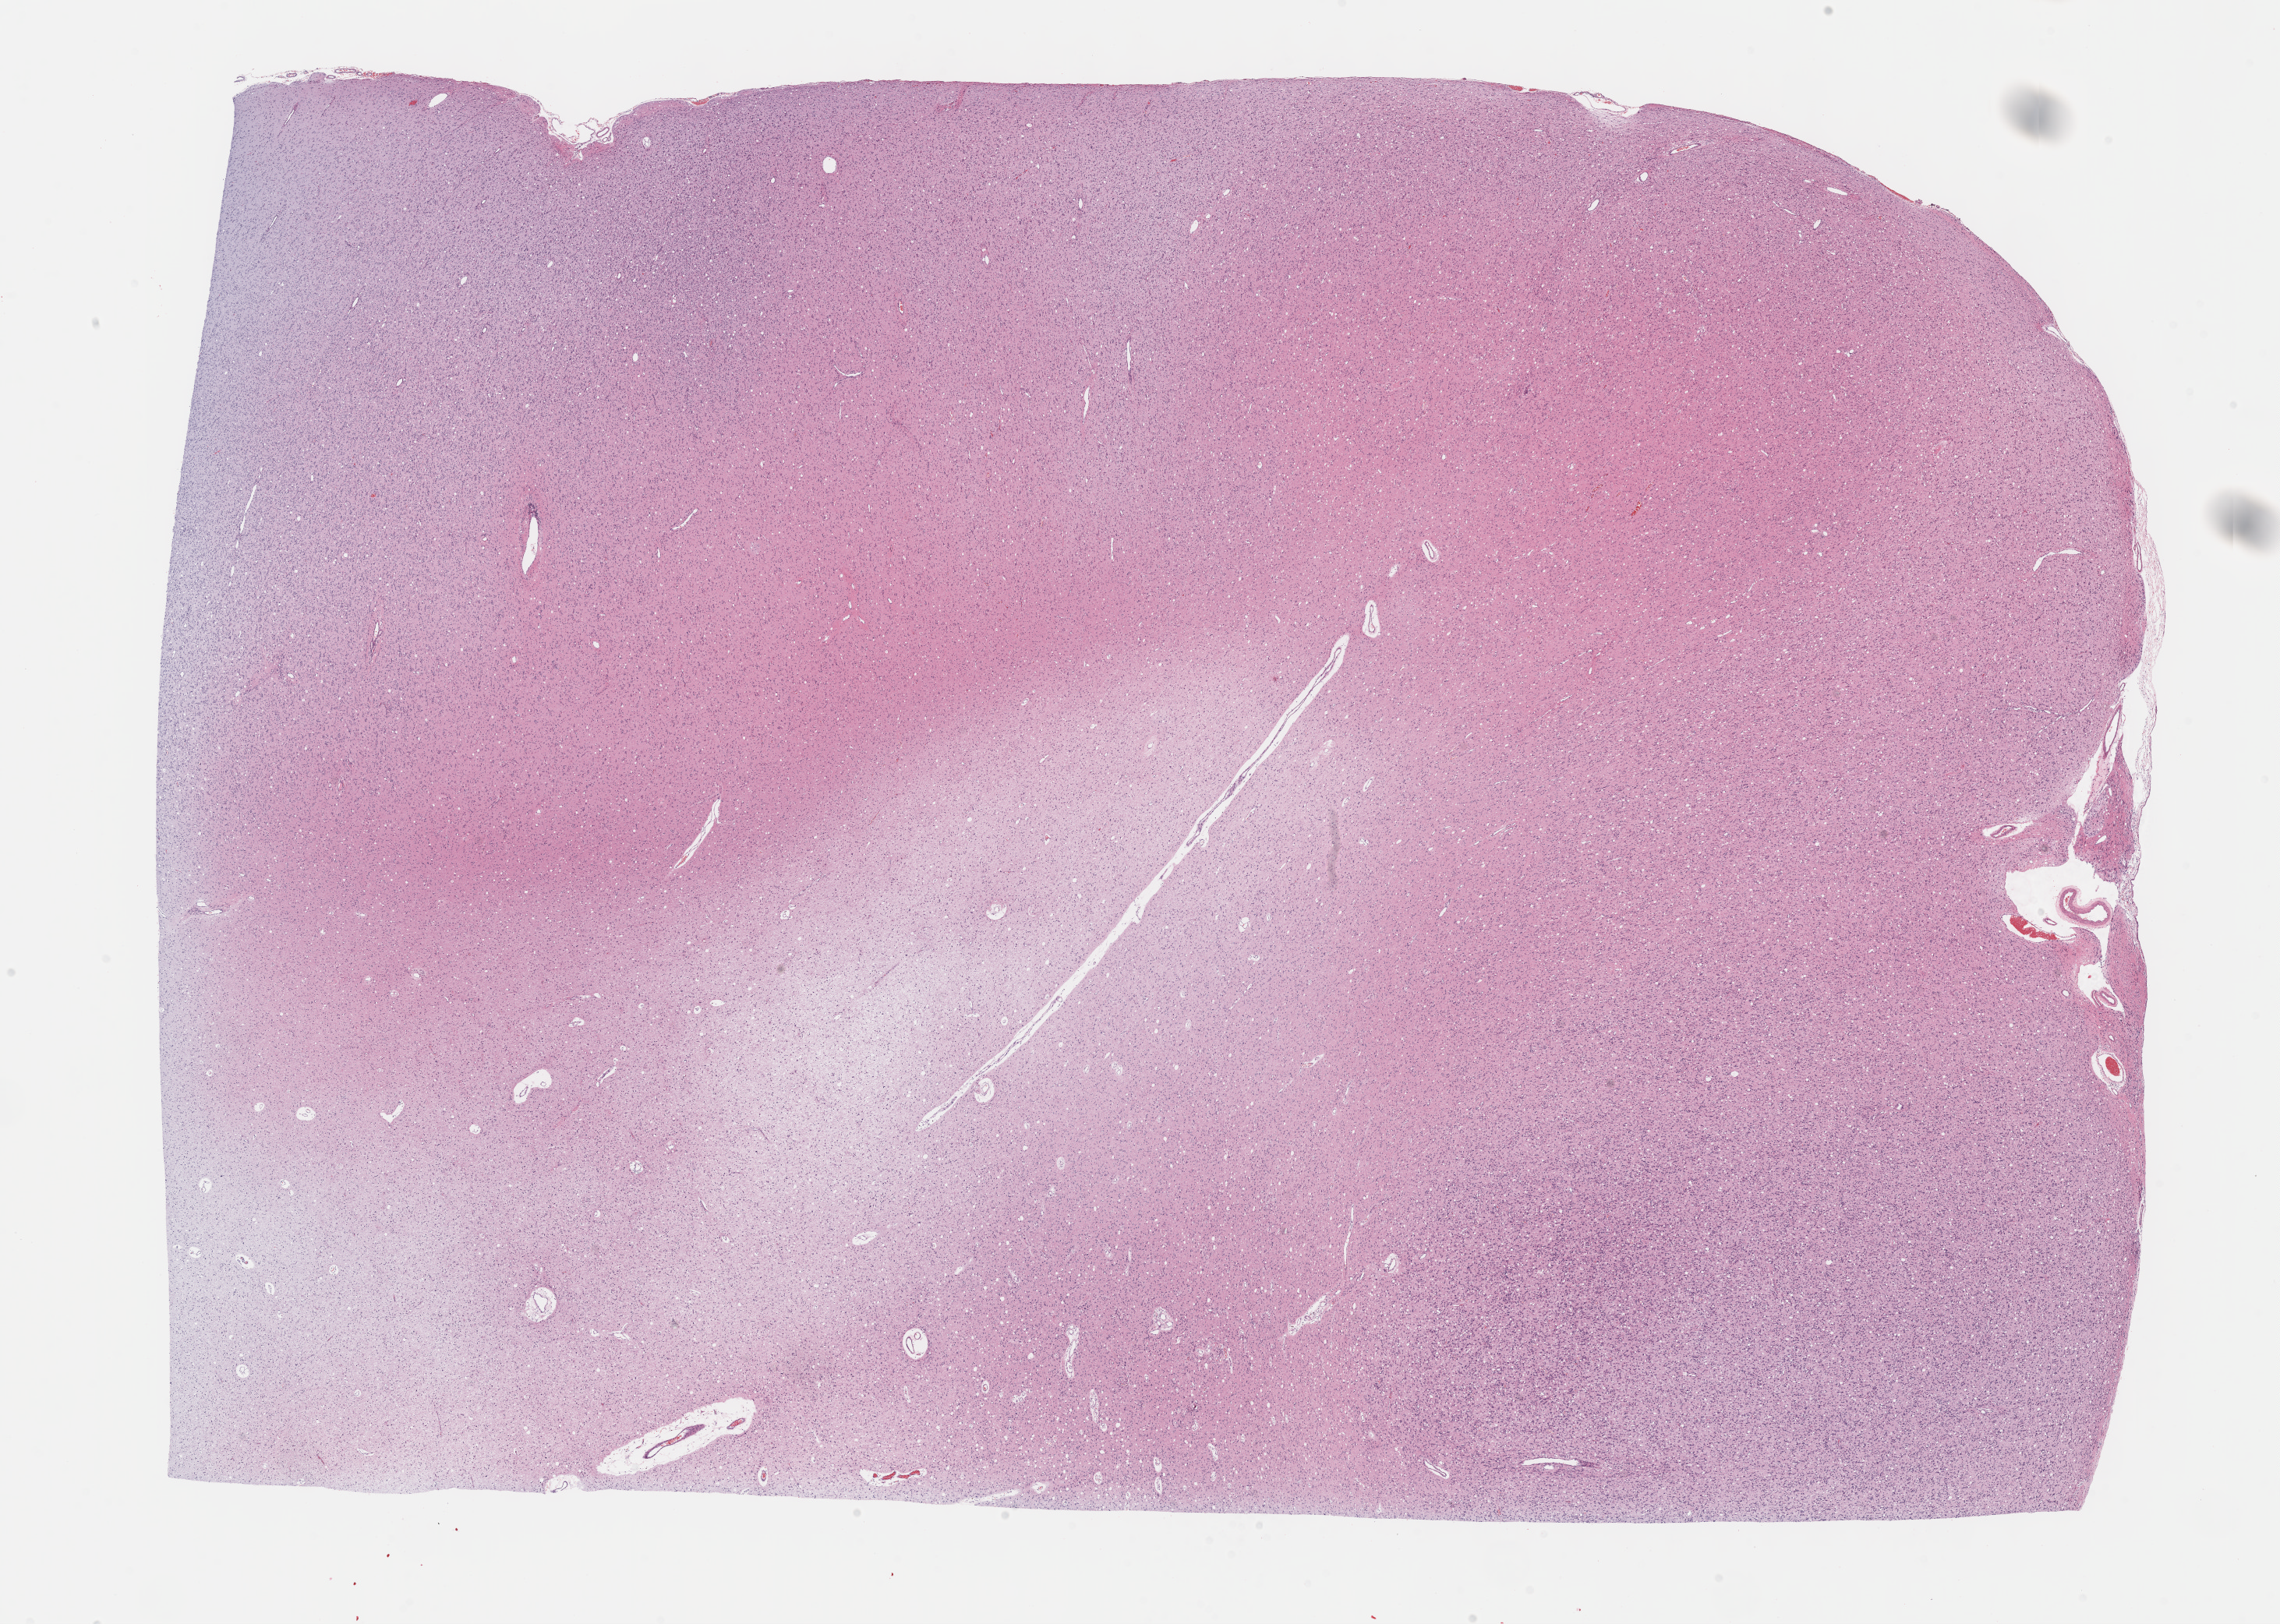
H&E-stained whole-slide image — whole scanned area (about 23.7 x 16.9 mm) shown as a low-resolution overview, formalin-fixed paraffin-embedded (FFPE) diagnostic section, sample: primary tumour, brain. Female, age 33 years at initial diagnosis.
Histologic diagnosis: Oligodendroglioma, NOS (cerebrum).